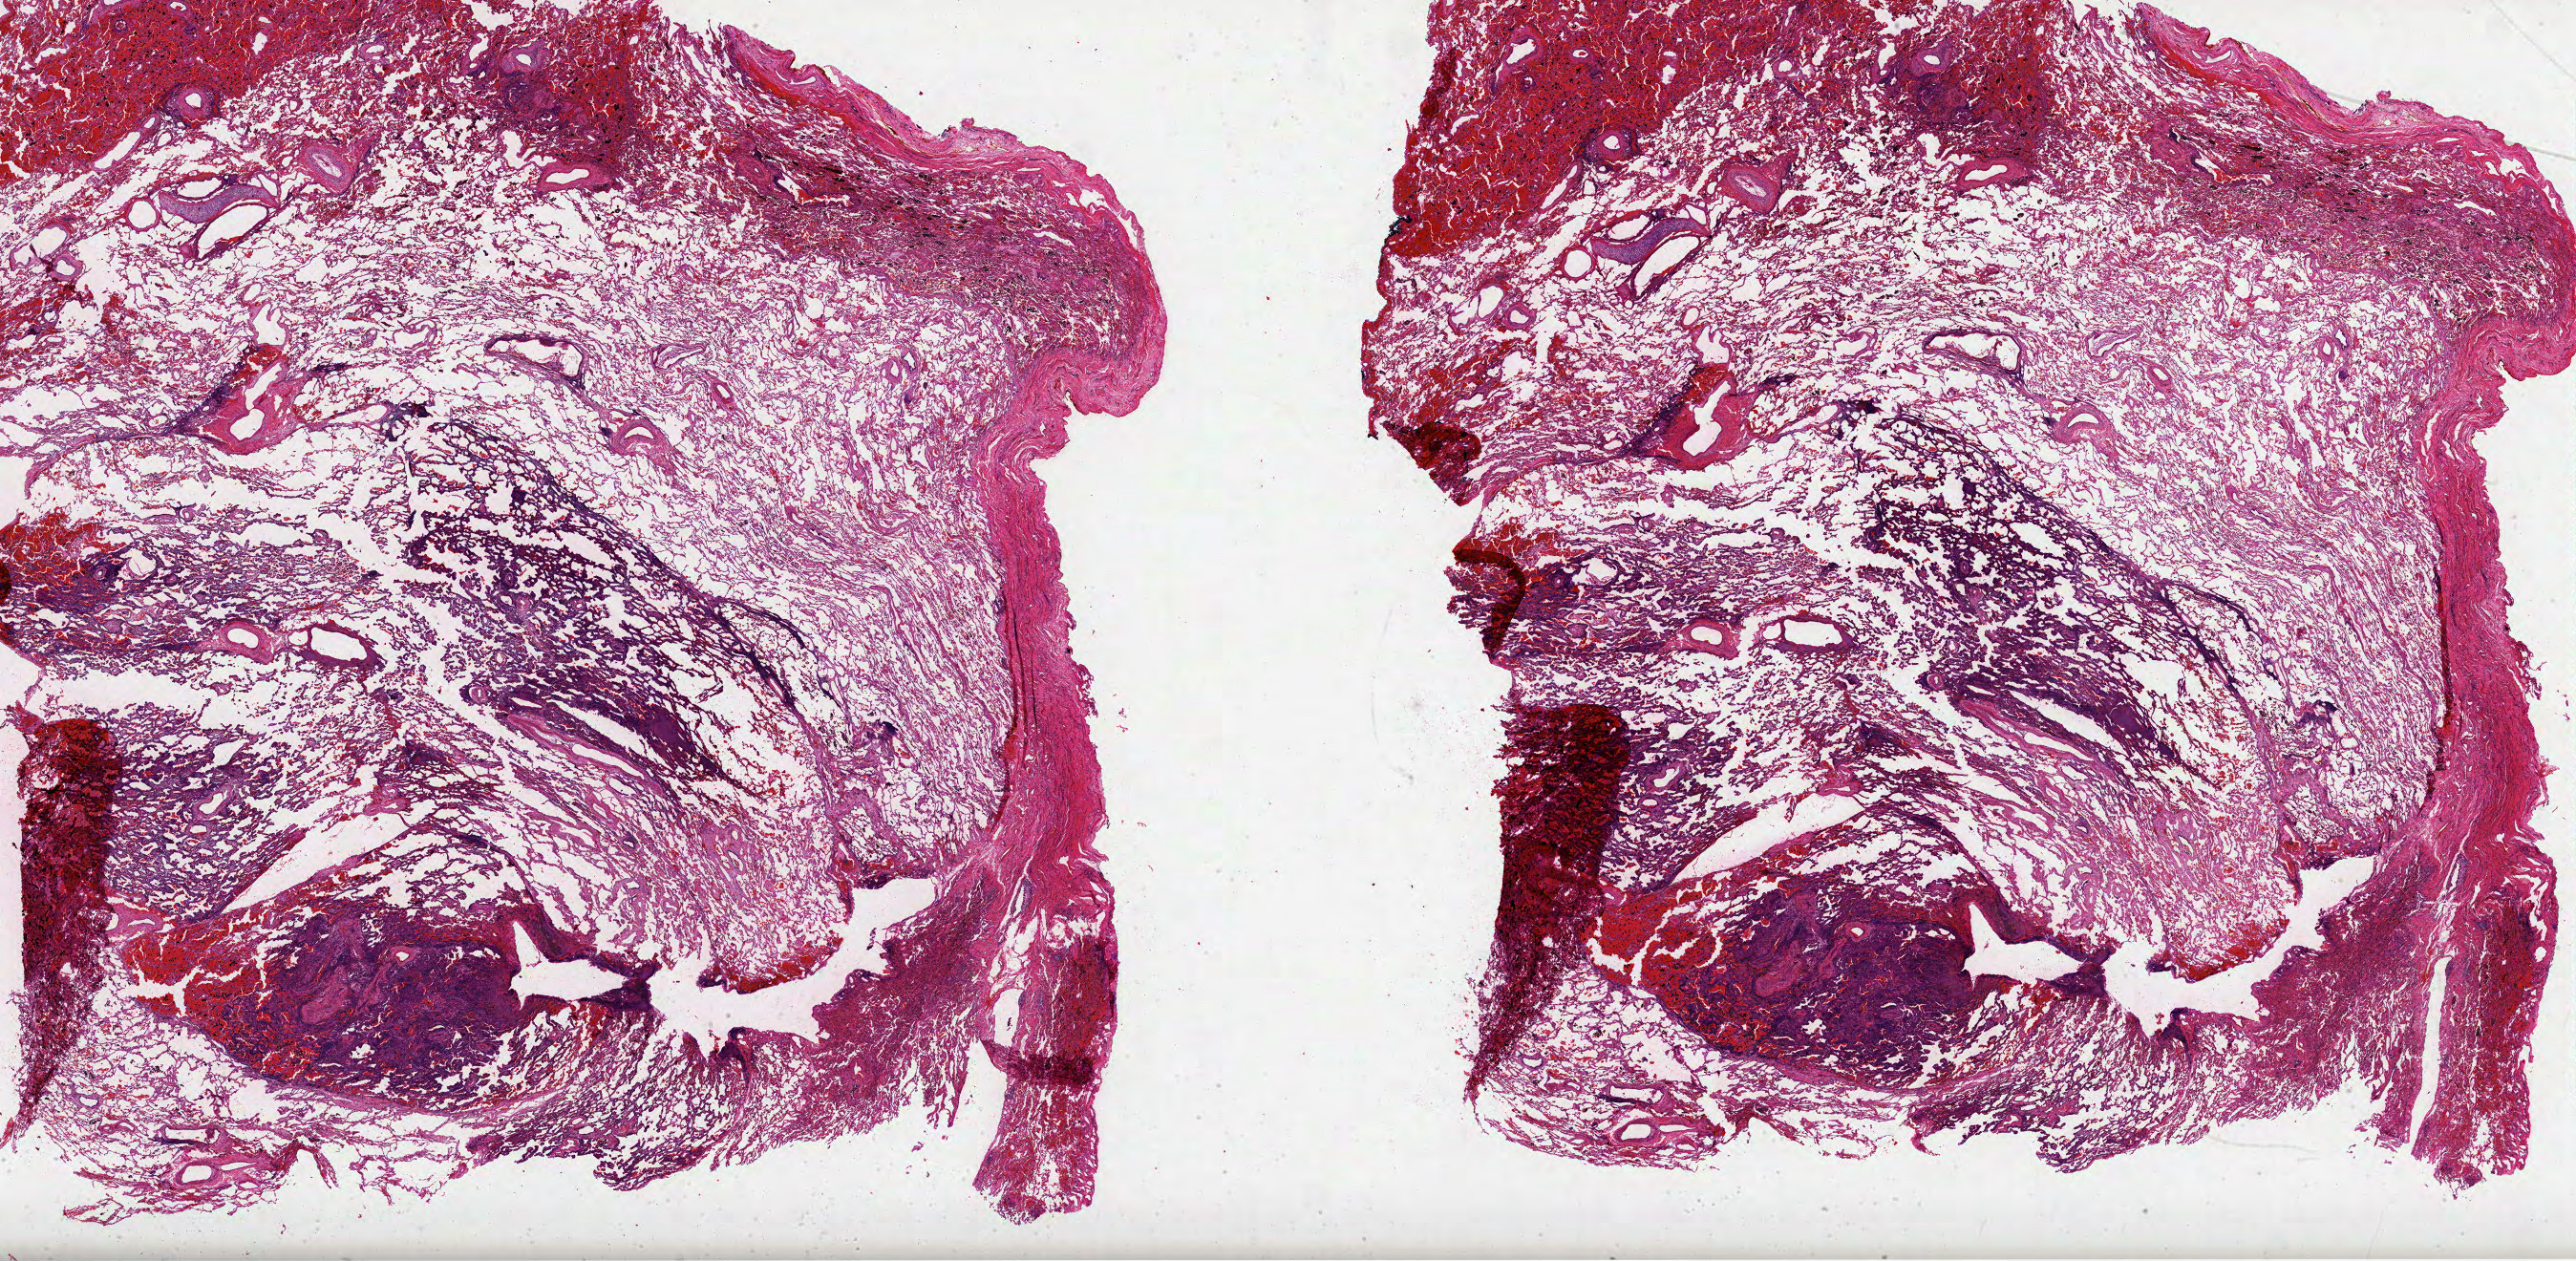
Hematoxylin and eosin (H&E) stained whole-slide image — low-resolution overview of the scanned area, about 43.5 x 21.3 mm. Formalin-fixed paraffin-embedded (FFPE) diagnostic section. Sample: primary tumour, lung. Female patient; age at initial diagnosis 64 years.
* laterality: left
* diagnosis: Adenocarcinoma with mixed subtypes
* AJCC pathologic stage: IIA (7th edition)